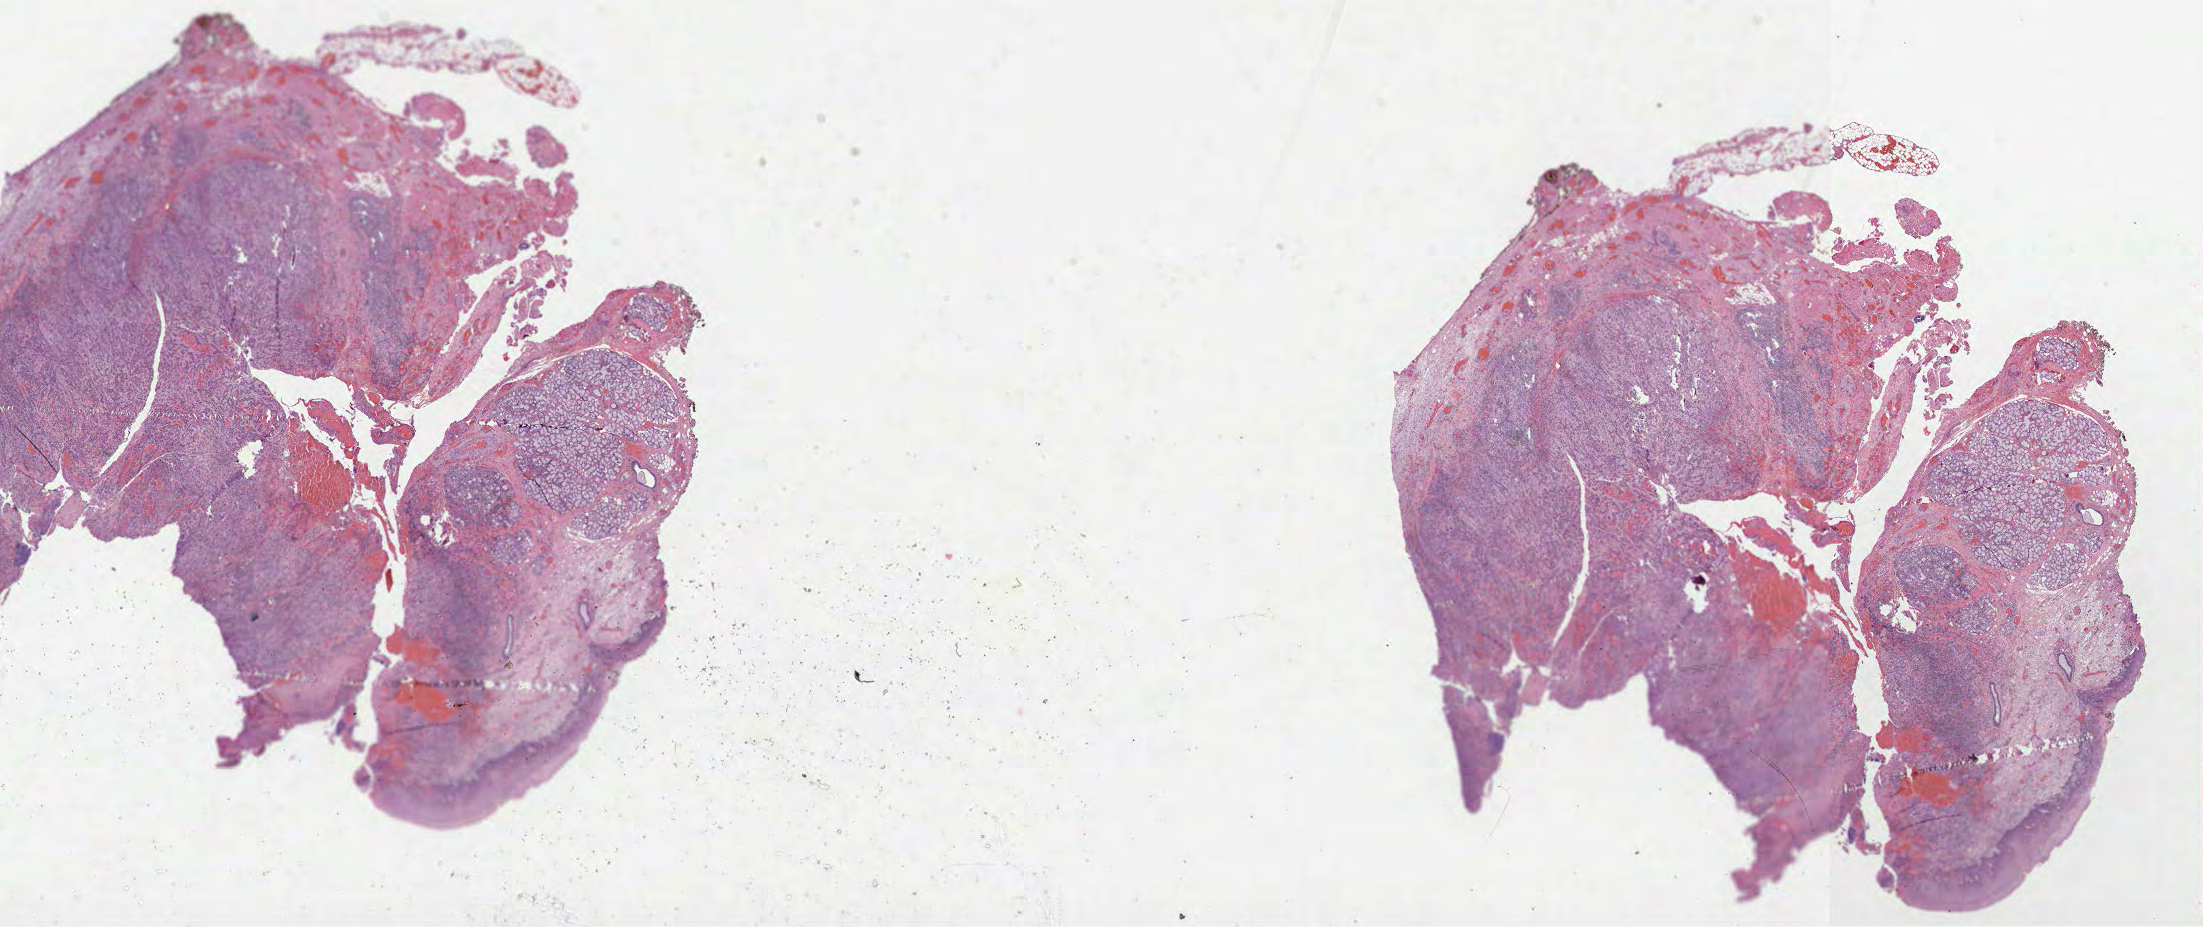
Whole-slide histology image, Hematoxylin and eosin (H&E) stained, low-resolution overview of the scanned area, about 35.5 x 15.0 mm (slide scanned at 40x); formalin-fixed paraffin-embedded (FFPE) diagnostic section; sample: primary tumour, head and neck. Male patient; age at initial diagnosis 49 years. Histologic grade: G3 (poorly differentiated).
Pathologic diagnosis: Squamous cell carcinoma, NOS (oropharynx, NOS). Lymph nodes positive (case pathology): 0 of 27 examined. Laterality: left. AJCC pathologic stage: II.